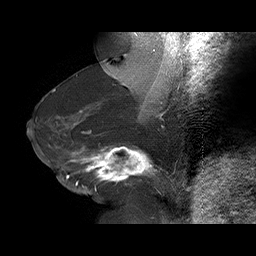
Breast MRI (dynamic contrast-enhanced), one sagittal slice. Slice 36 of 75 in the series (ordered by position). Dynamic contrast-enhanced series, time point 2 of 6 at this slice position (early post-contrast). 1.5 T. TE 4.5 ms, TR 32.4 ms. 3 mm slice thickness. 256 × 256 image matrix. Female patient. From the clinical record (not read from this slice): setting: breast cancer imaged before/during neoadjuvant chemotherapy; receptor status: HR-positive, HER2-negative.
Outlined on this slice (semi-automatic segmentation, software-assisted and operator-edited):
- analysis volume of interest (the breast-tissue region the enhancement analysis was run in; not a lesion): bounding box (x1, y1, x2, y2) in pixels: (58, 134, 166, 191)
- tumour enhancement mask (voxels above the 100 % enhancement threshold inside the analysis volume of interest): (62, 146, 157, 190)